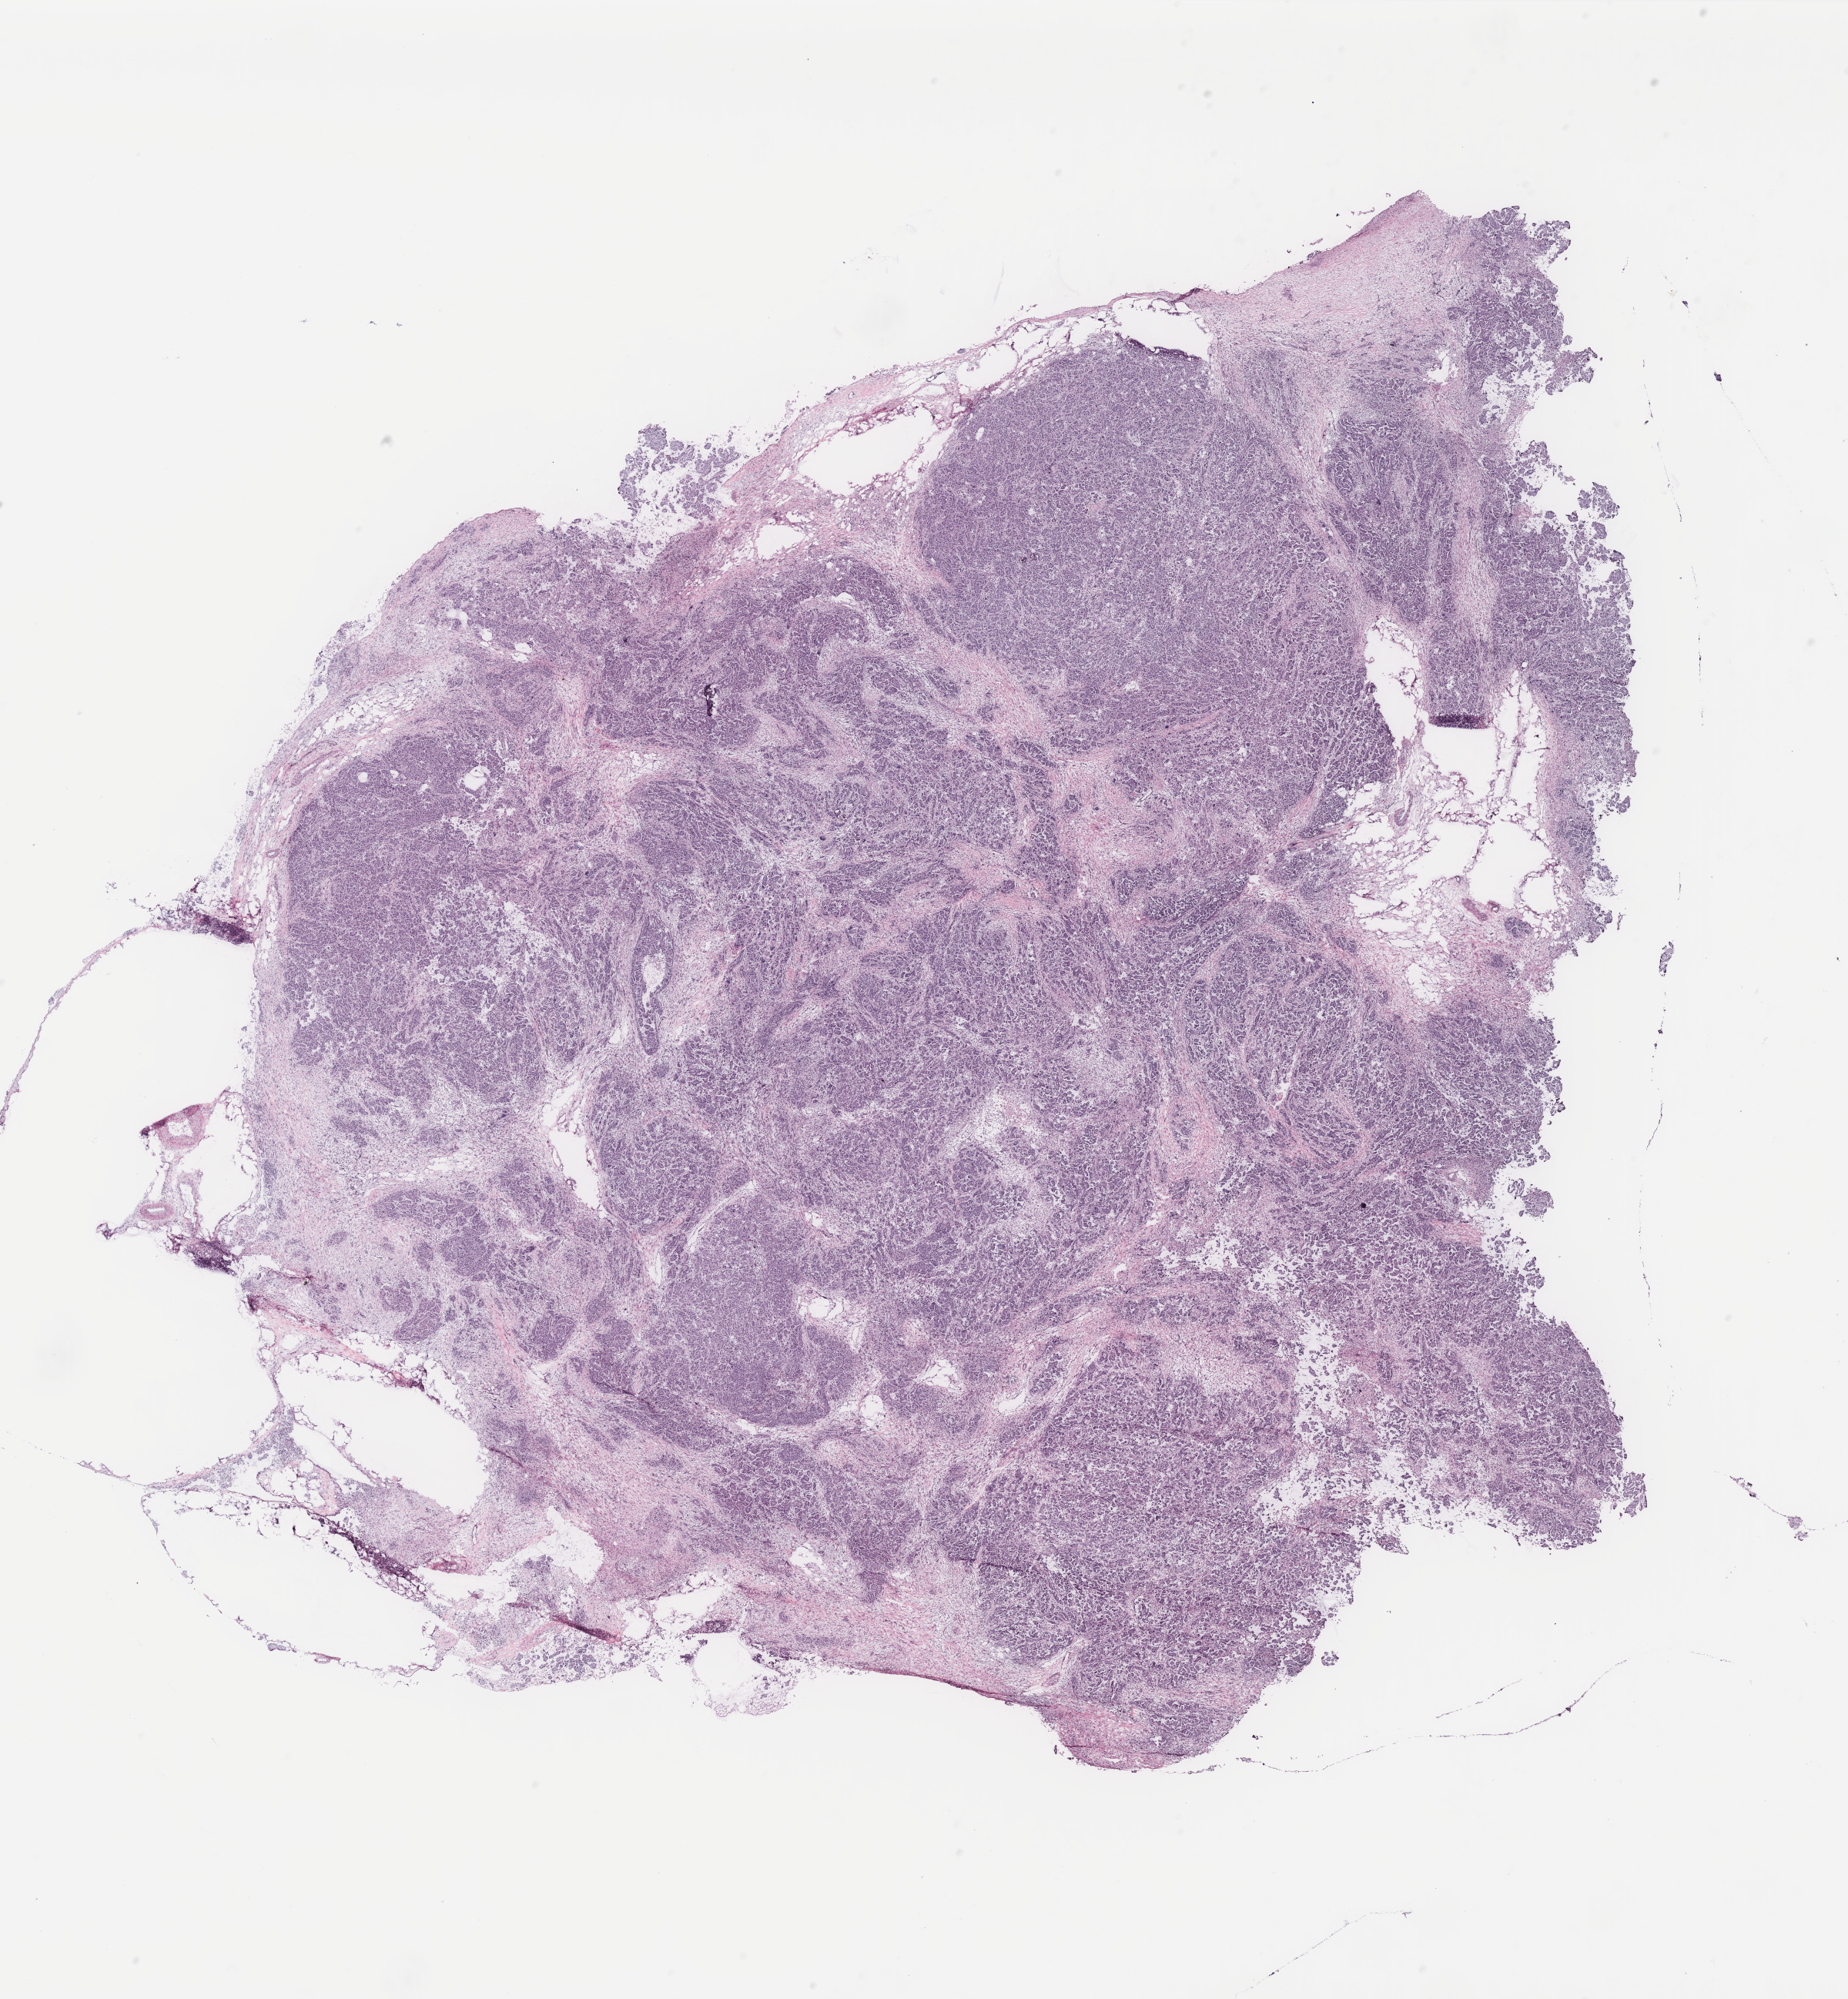
Digitized Hematoxylin and eosin (H&E) stained tissue section (whole slide) — low-resolution overview of the scanned area, about 19.2 x 20.8 mm (from a 40x scan), ovary, tumour tissue. Female, 59 y/o.
Diagnosis: Serous adenocarcinoma, NOS. Primary tumour site (as recorded): ovary.